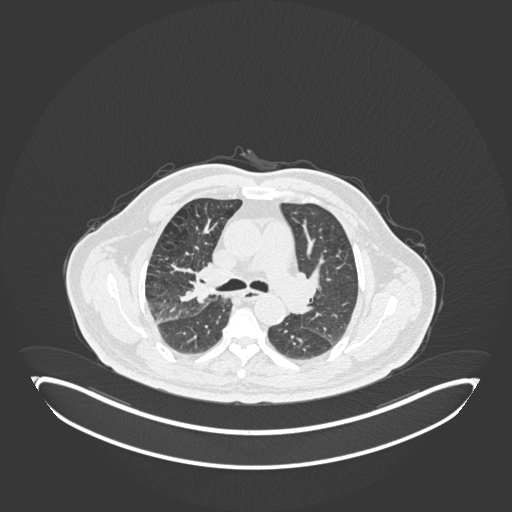
Chest CT, one axial slice; position 112 of 247 along the scan axis; reconstruction kernel B30f; lung window (W 1500 / L -600 HU); 512 × 512 image matrix. Patient: male, 72 years. From the clinical record (not read from this slice): clinical TNM (as recorded): T1c N0 M0; histopathological grade: G2.
Structures marked on this image (bounding box drawn by a radiologist):
- lung tumour (recorded histology: squamous cell carcinoma): bounding box <182,264,219,313> (left, top, right, bottom; pixels)